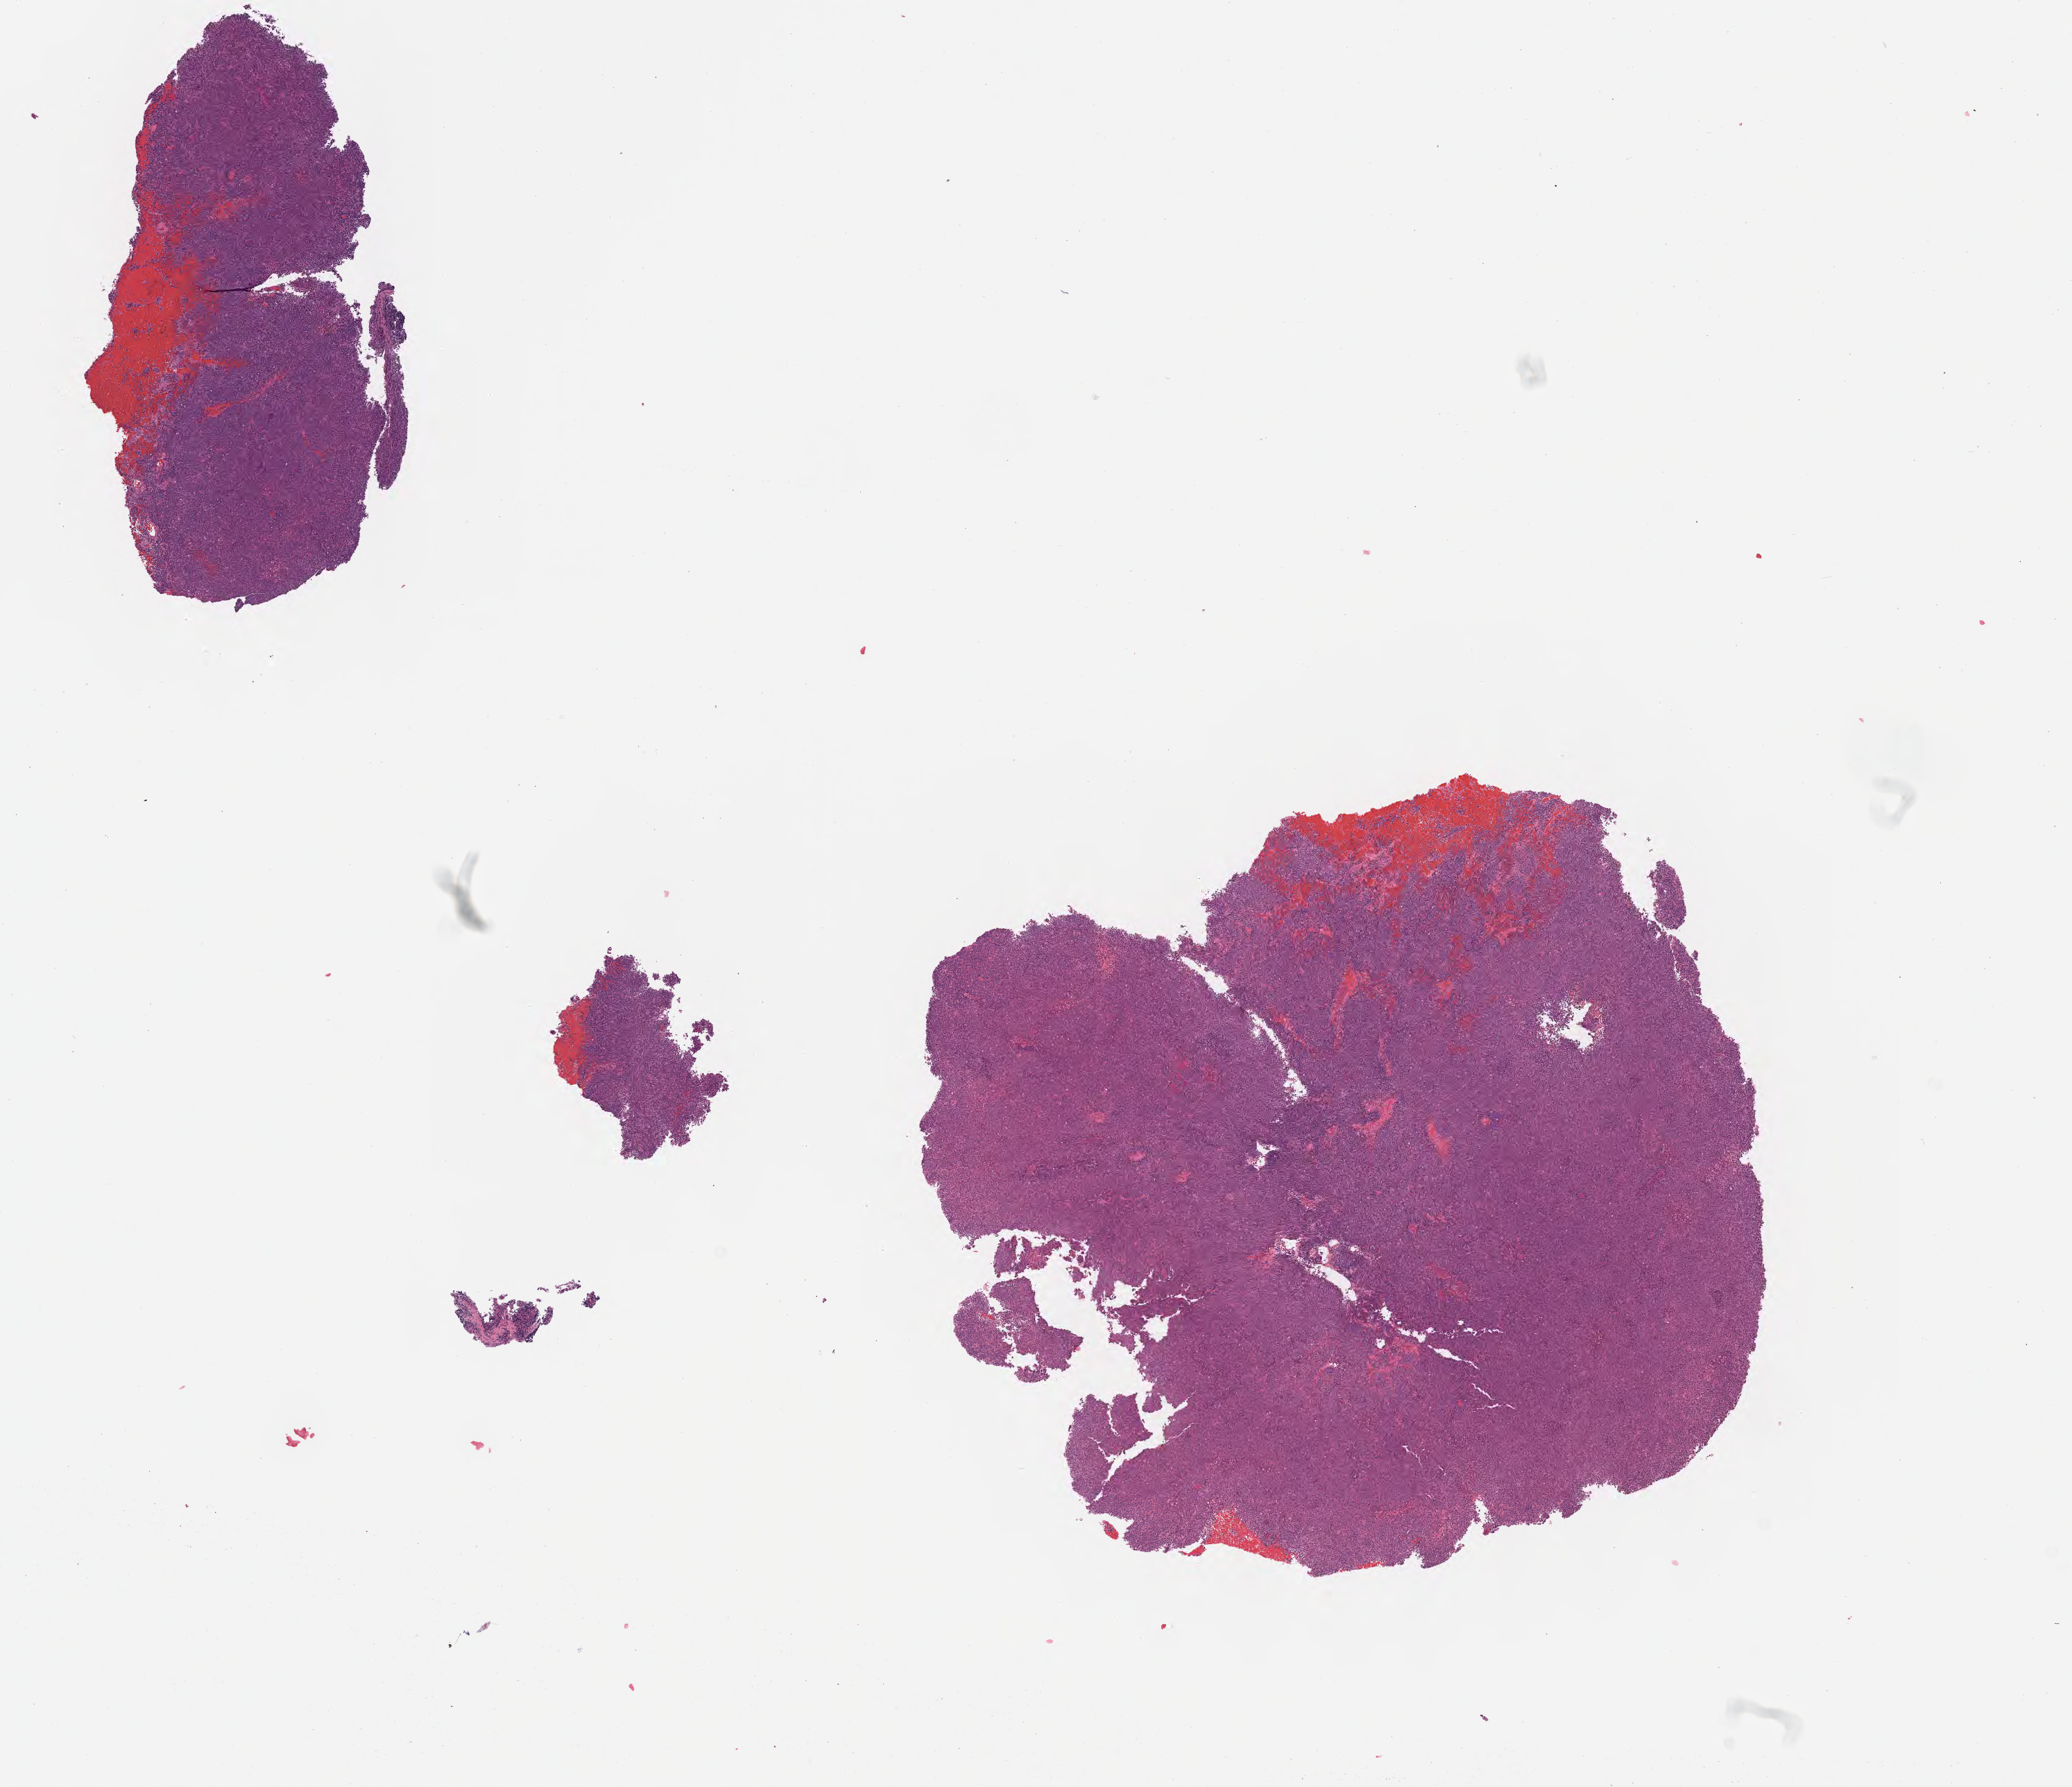
Hematoxylin and eosin (H&E) whole-slide image, a low-resolution overview of the entire scanned area, about 12.1 x 10.4 mm; tumor tissue; anatomic site: lymph node. Patient female; 51 years old.
Histologic diagnosis: Diffuse large B-cell lymphoma, NOS.